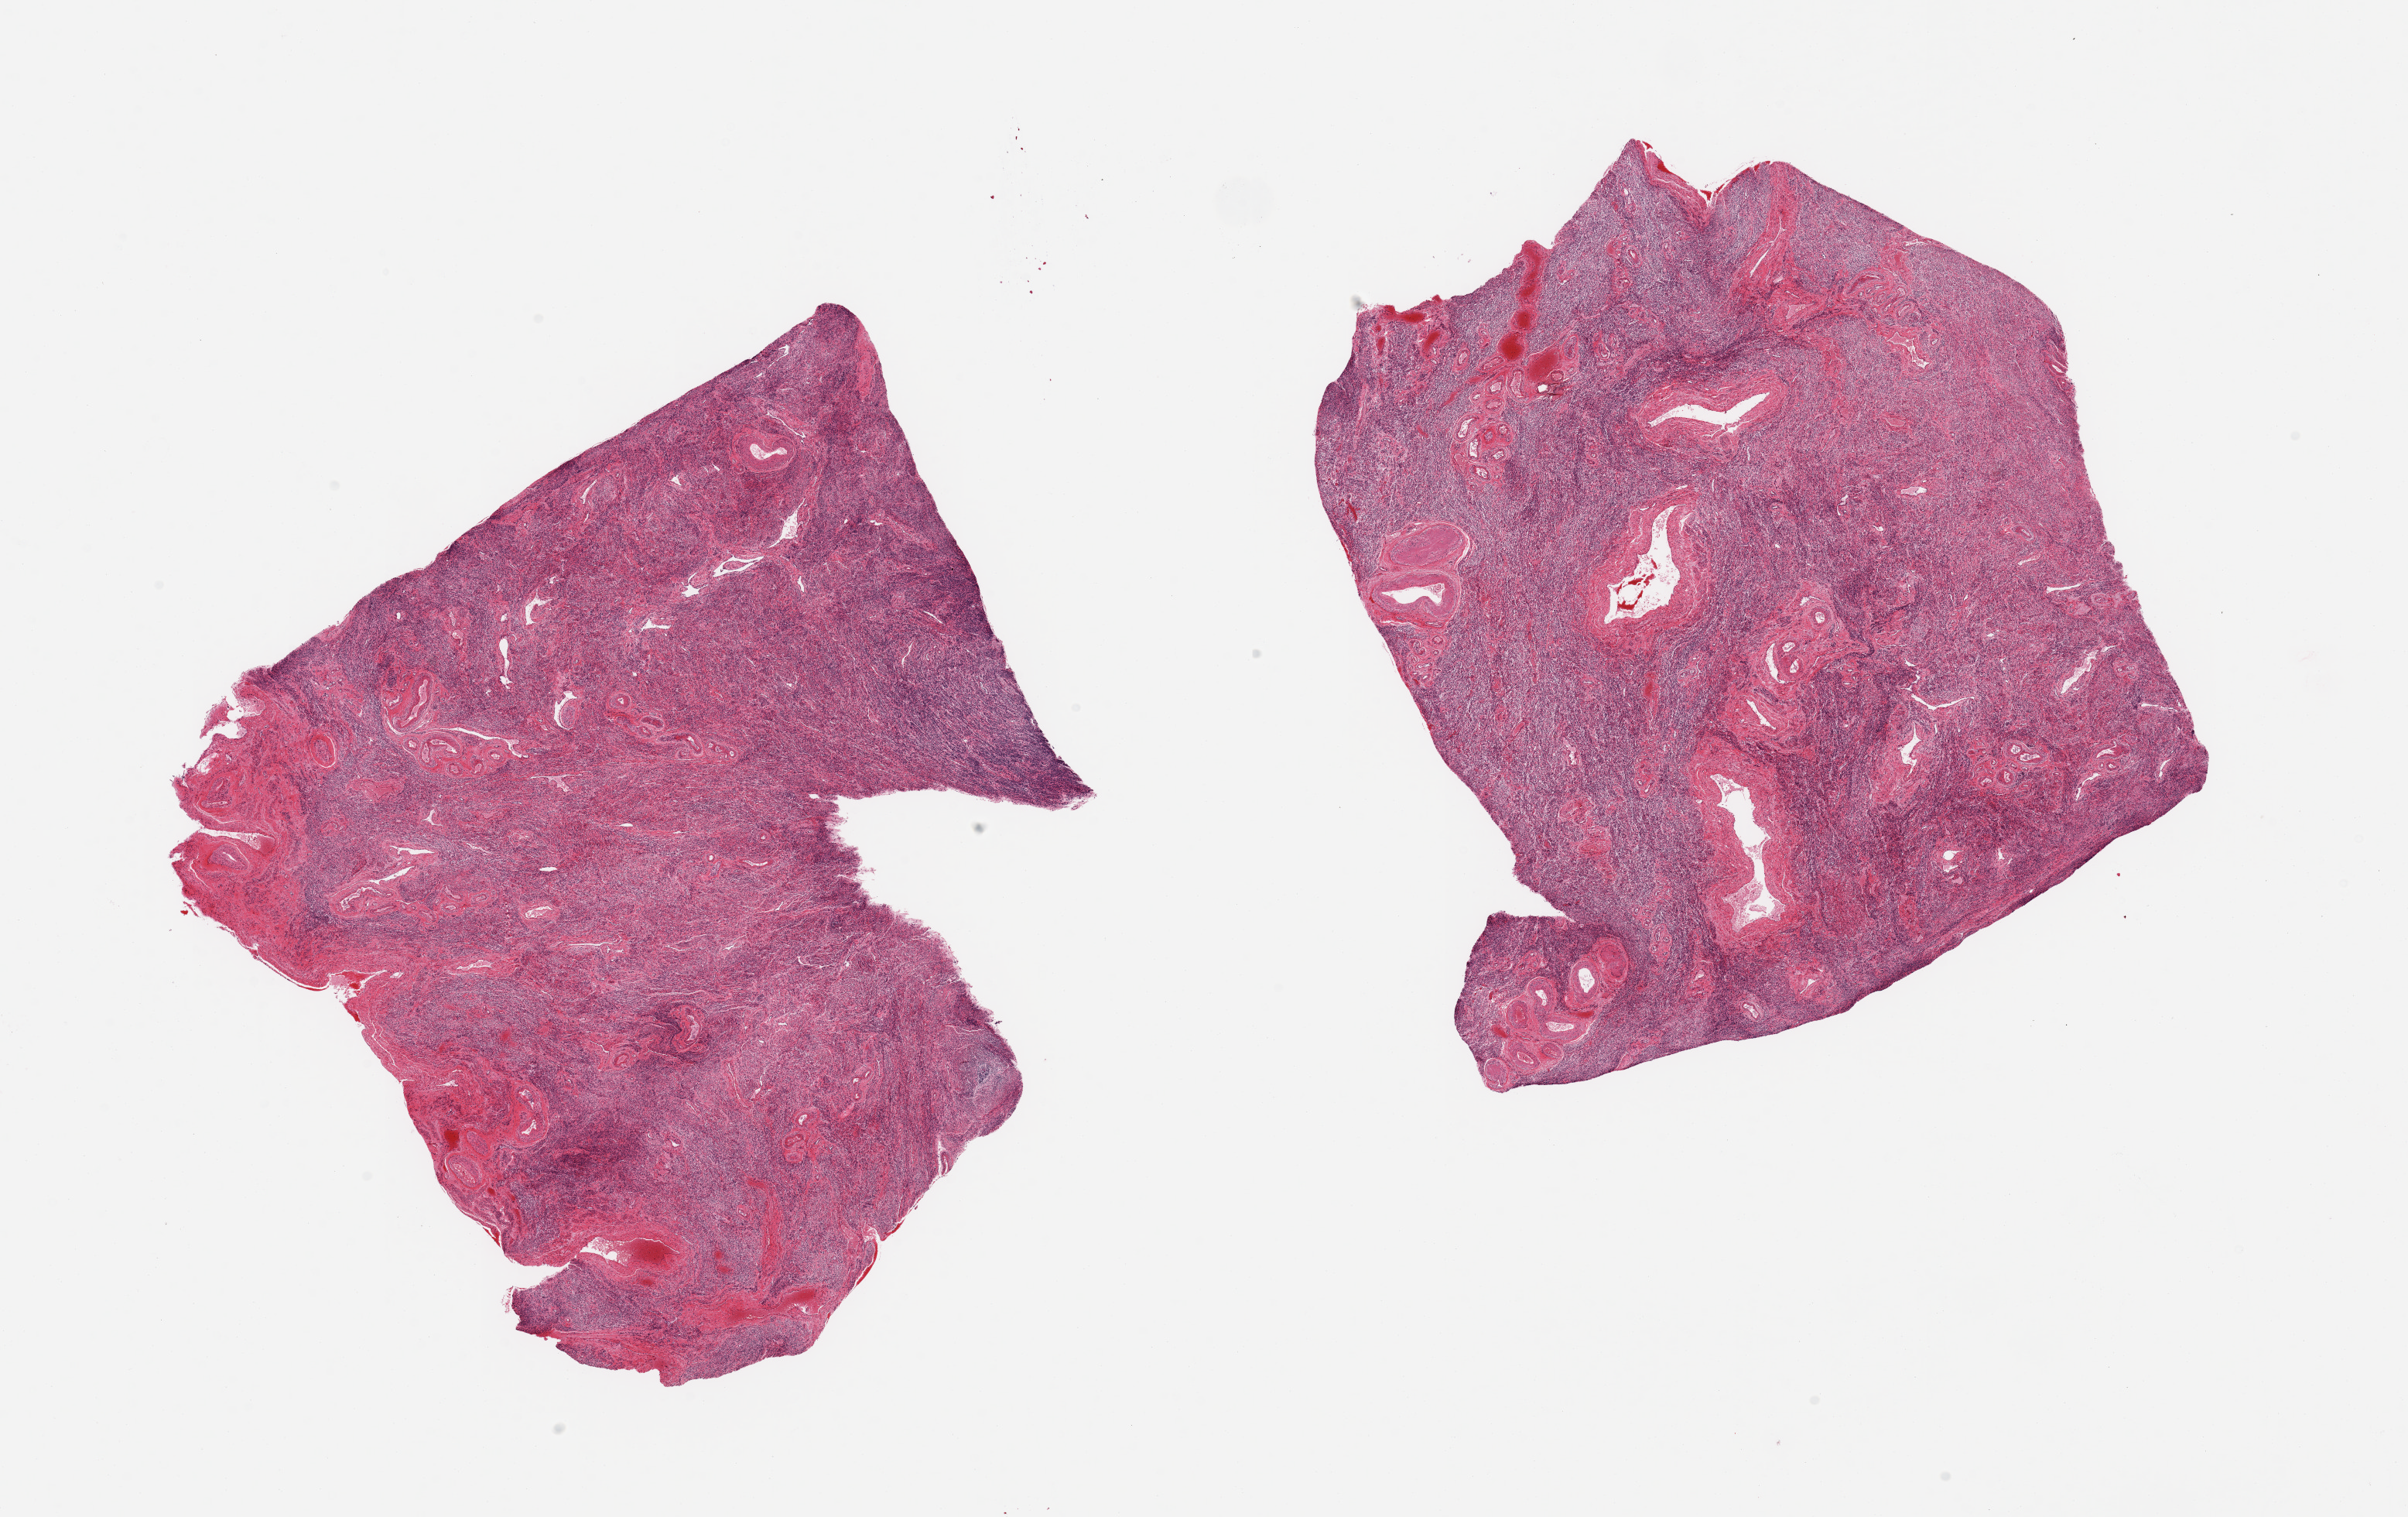
Whole-slide image, haematoxylin and eosin stain, a low-resolution overview of the entire scanned area, about 24.6 x 15.5 mm, PAXgene-fixed paraffin-embedded (PFPE) section, section of uterus (target tissue), donor tissue sample. Donor sex: female.
Reviewer comment on this tissue sample: 2 pieces; no glandular component.